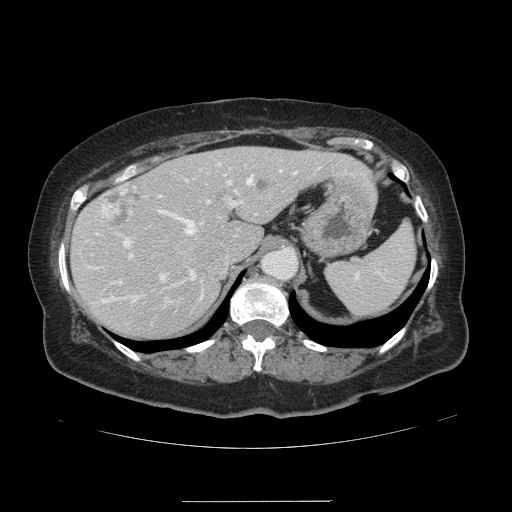
Contrast-enhanced abdominal CT, one axial slice. Slice 93 of 141 in the series (ordered by position). 120 kVp. Intravenous contrast given. Soft-tissue window (W 400 / L 40 HU). 2.5 mm slice thickness. 512 × 512 image matrix. Female patient, age 74 years. From the clinical record (not read from this slice): diagnosis: colorectal cancer liver metastases, imaged before liver resection; multiple liver metastases: yes.
Annotated regions visible in this slice (manually delineated by an expert):
- hepatic veins: bounding box [x1, y1, x2, y2] px = [131, 170, 281, 298]
- liver: [72, 148, 368, 340]
- planned liver remnant (the part of the liver to remain after resection): [72, 148, 368, 340]
- portal vein (with intrahepatic branches): [117, 162, 296, 302]
- liver metastasis: [259, 182, 266, 188]
- liver metastasis: [101, 184, 140, 228]